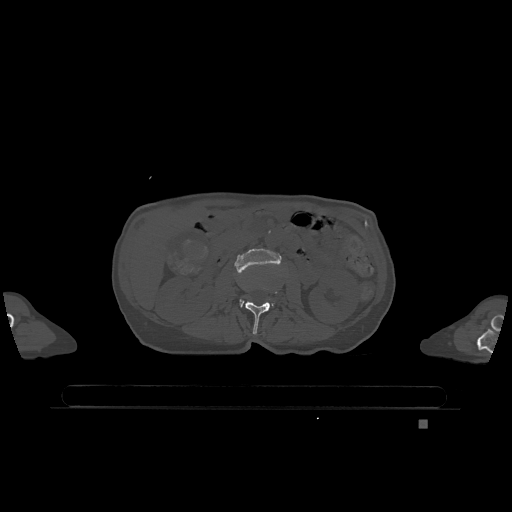
CT including the spine, one axial slice; slice 396 of 1317 in the series (ordered by position); bone window (W 1800 / L 400 HU); 0.5 mm slice thickness; 512 × 512 image matrix, field of view 500 × 500 mm. Patient: female, 74 years. From the clinical record (not read from this slice): primary cancer: lung.
Outlined on this slice (semi-automatically segmented with operator editing):
- L2 vertebra: bounding box [x1, y1, x2, y2] px = [245, 288, 278, 335]
- L3 vertebra: [235, 248, 281, 306]